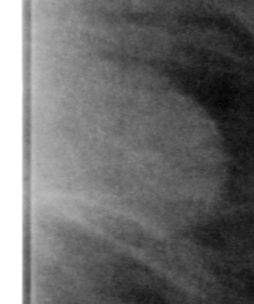
Crop from a digitized film mammogram around one marked abnormality, right breast, MLO view, BI-RADS breast density category 4 (scale 1–4).
Mass, shape oval, margins obscured; BI-RADS assessment category 3; subtlety rating 3 on a 1 (subtle) to 5 (obvious) scale; pathology result (as recorded, not read from the image): benign.